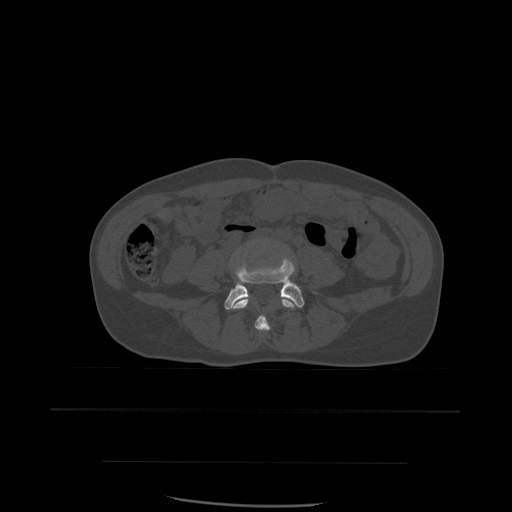
CT including the spine, one axial slice; slice 158 of 574 in the series (ordered by position); bone window (W 1800 / L 400 HU); 512 × 512 image matrix, field of view 392 × 392 mm. Patient age 48 years. Case-level facts recorded for this patient, not image findings: primary cancer: lung; vertebrae with lytic lesions (as recorded): T11.
Outlined on this slice (semi-automatically segmented with operator editing):
- L4 vertebra: box from (x=231, y=296) to (x=297, y=332) px
- L5 vertebra: (x=225, y=259)–(x=304, y=310)